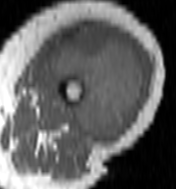
MRI of an extremity soft-tissue mass, one axial slice. Position 52 of 100 along the scan axis. MR volume resampled by the dataset authors to the PET/CT grid (not the native acquisition matrix). 176 × 189 image matrix. Female patient. From the clinical record (not read from this slice): histological type: undifferentiated – high grade; grade: high; site of the primary tumour: left thigh.
Structures marked on this image (expert contour drawn on MRI and transferred to this co-registered scan by the dataset authors):
- gross tumour volume including surrounding oedema: bounding box <50,25,147,143> (left, top, right, bottom; pixels)
- gross tumour volume (mass): <50,25,145,143>